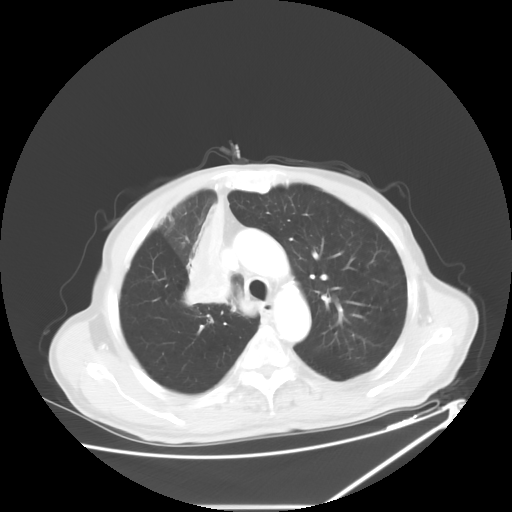
Chest CT, one axial slice; slice 44 of 60 in the series (ordered by position); reconstruction kernel STANDARD; 120 kVp; lung window (W 1500 / L -600 HU); 5 mm slice thickness; 512 × 512 image matrix, field of view 410 × 410 mm. Patient: male, 73 years. From the clinical record (not read from this slice): clinical TNM (as recorded): T2a N1 M0.
Annotated regions visible in this slice (bounding box drawn by a radiologist):
- lung tumour (recorded histology: squamous cell carcinoma): bounding box (x1, y1, x2, y2) in pixels: (181, 191, 237, 312)